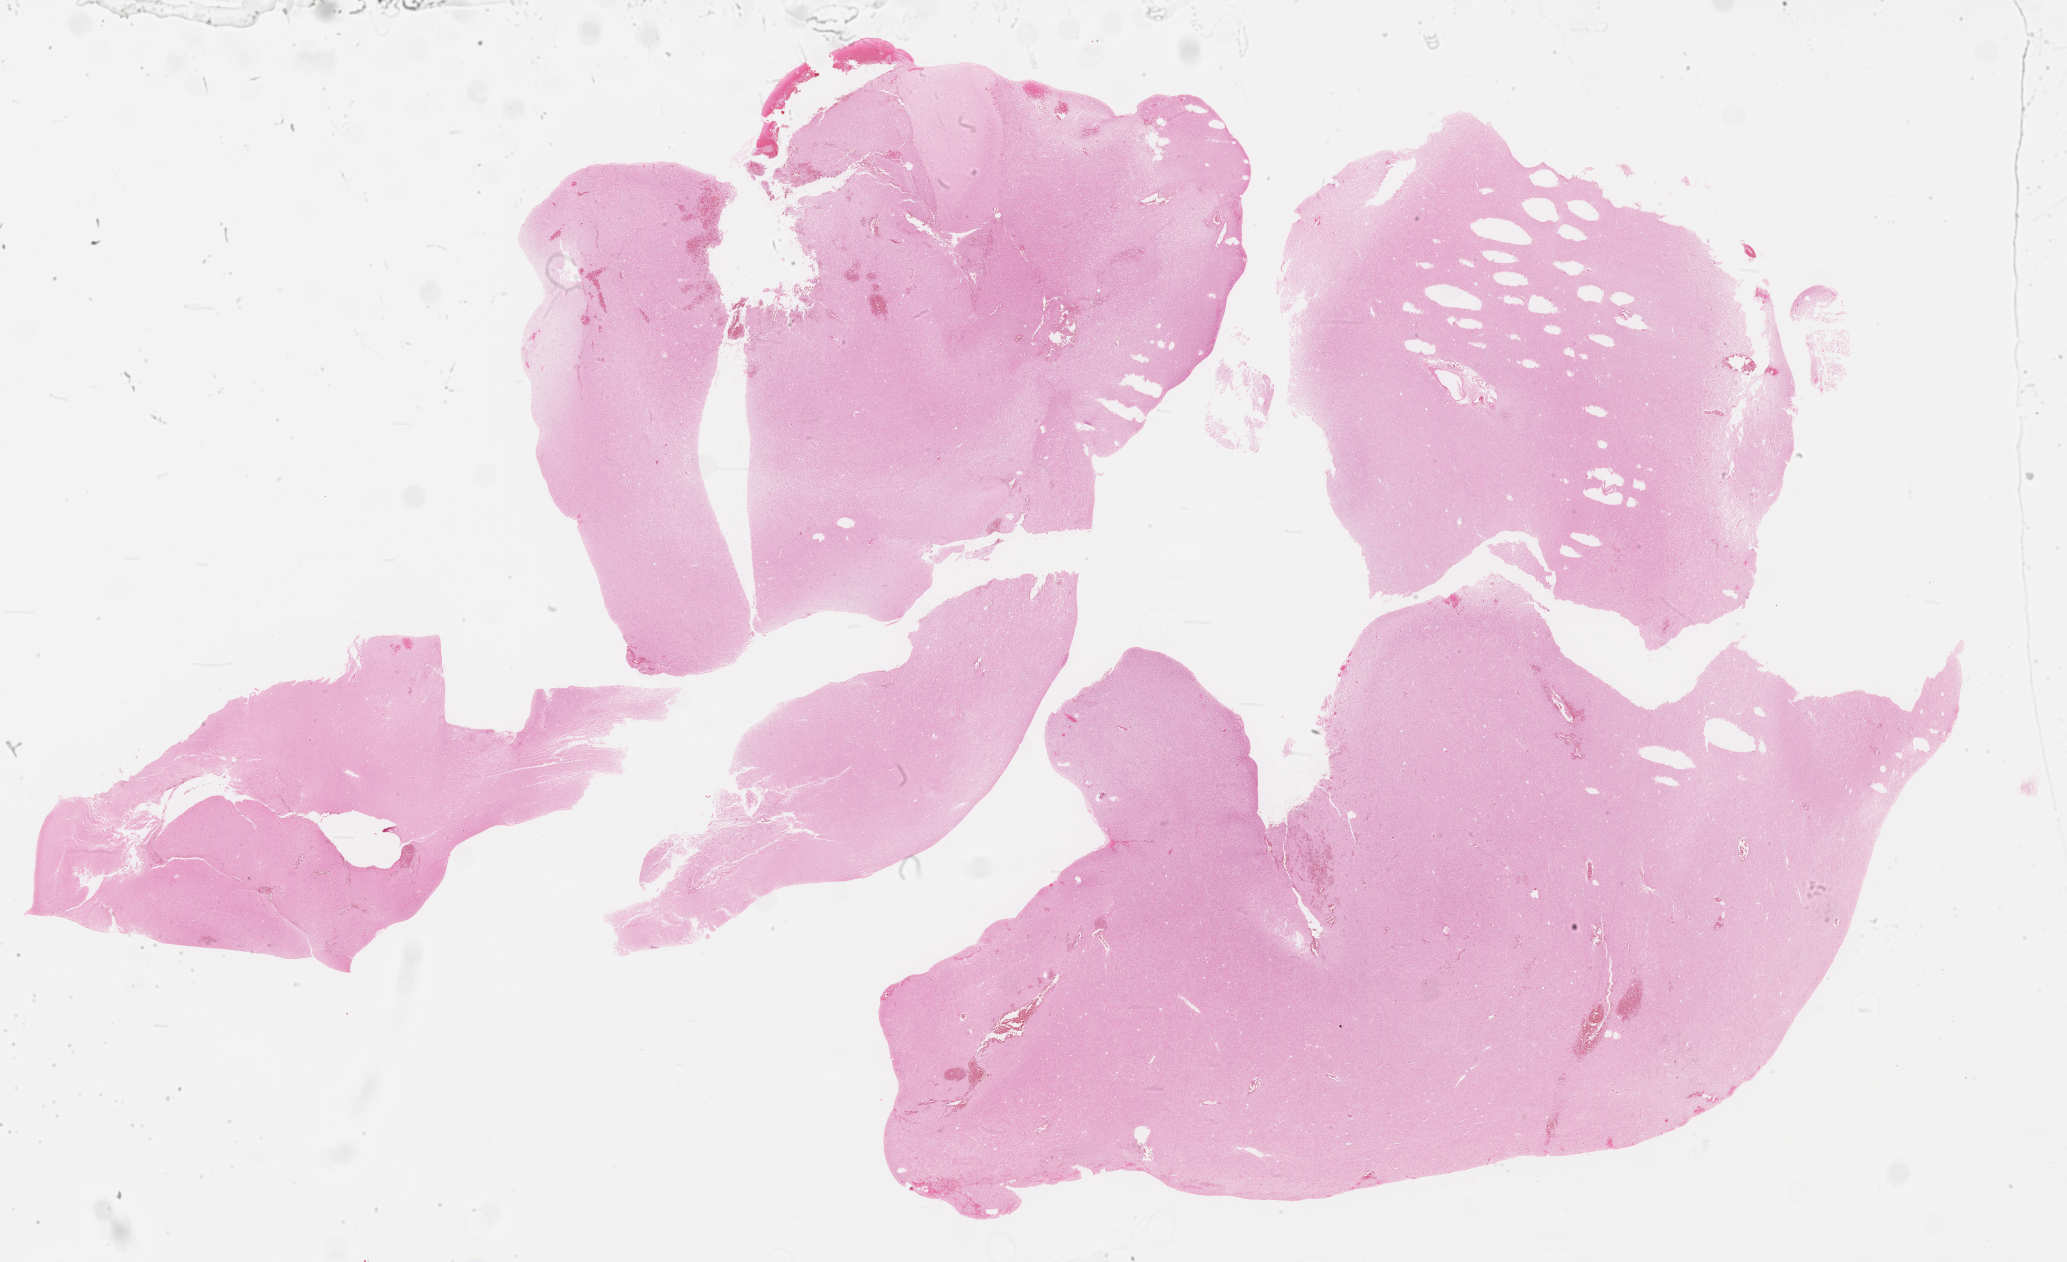
Digitized Hematoxylin and eosin (H&E) stained tissue section (whole slide) — whole scanned area (about 33.3 x 20.3 mm, from a 40x scan) shown as a low-resolution overview. Formalin-fixed paraffin-embedded (FFPE) diagnostic section. Brain, primary tumour sample. Patient: male, age at initial diagnosis 40 years. Histologic grade: G2 (moderately differentiated).
Diagnosis: Oligodendroglioma, NOS.